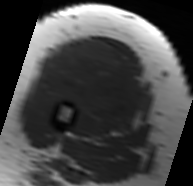
MRI of an extremity soft-tissue mass, one axial slice. Position 31 of 91 along the scan axis. MR volume resampled by the dataset authors to the PET/CT grid (not the native acquisition matrix). 3.27 mm slice thickness. 193 × 186 image matrix. Female patient. Case-level facts recorded for this patient, not image findings: histological type: malignant solitary fibrous tumor; grade: intermediate; site of the primary tumour: right thigh.
Structures marked on this image (expert contour drawn on MRI and transferred to this co-registered scan by the dataset authors):
- gross tumour volume including surrounding oedema: bounding box [x1, y1, x2, y2] px = [38, 39, 148, 127]
- gross tumour volume (mass): [44, 39, 144, 123]